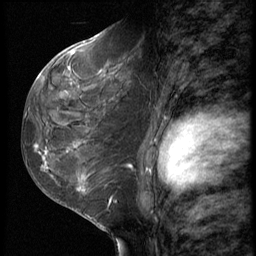
Breast MRI (dynamic contrast-enhanced), one sagittal slice; position 35 of 62 along the scan axis; 3 images stored at this slice position (order not interpretable as contrast timing); 1.5 T; TE 4.2 ms, TR 9 ms; 2.5 mm slice thickness; 256 × 256 image matrix. Patient: female, 50 years. Case-level facts recorded for this patient, not image findings: setting: breast cancer imaged before/during neoadjuvant chemotherapy; receptor status: HR-positive, HER2-negative.
Annotated regions visible in this slice (semi-automatic segmentation, software-assisted and operator-edited):
- analysis volume of interest (the breast-tissue region the enhancement analysis was run in; not a lesion): bounding box (x1, y1, x2, y2) in pixels: (32, 91, 118, 209)
- tumour enhancement mask (voxels above the 140 % enhancement threshold inside the analysis volume of interest): (36, 145, 113, 200)